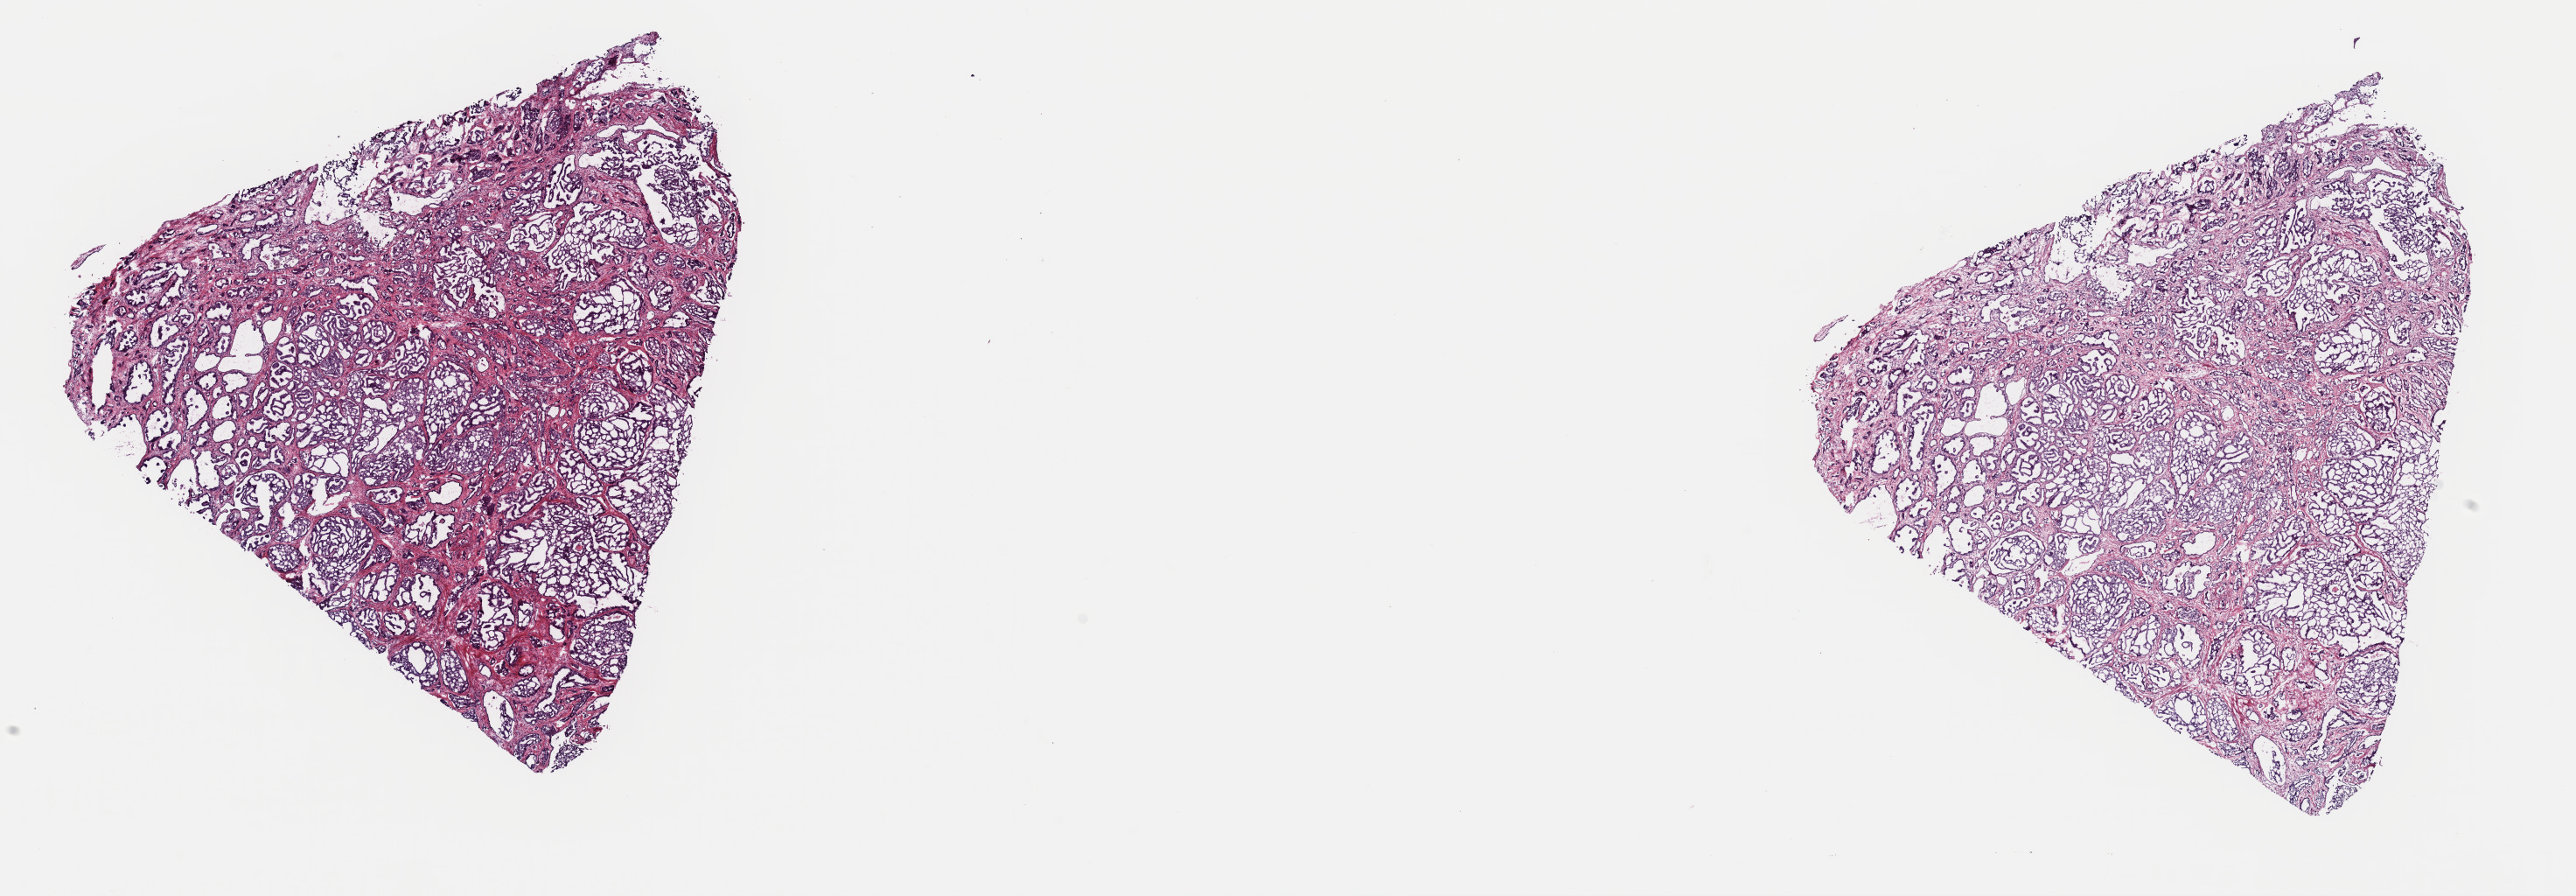
Whole-slide histology image, Hematoxylin and eosin (H&E) stained — whole scanned area (about 23.3 x 8.1 mm, from a 40x scan) shown as a low-resolution overview. Frozen section from the top of the tissue portion. Sample: primary tumour, prostate. Patient: male, age at initial diagnosis 63 years. Gleason score: 9 (4+5). Slide review estimates, as recorded: tumour cells 70%, tumour nuclei 80%, normal cells 0%, stromal cells 30%, necrosis 0%. Infiltration values recorded for this section: lymphocyte infiltration 0%, monocyte infiltration 0%, neutrophil infiltration 0%.
Histologic diagnosis: Adenocarcinoma, NOS (prostate gland). Laterality: bilateral. Lymph nodes positive (case pathology): 3 of 11 examined.